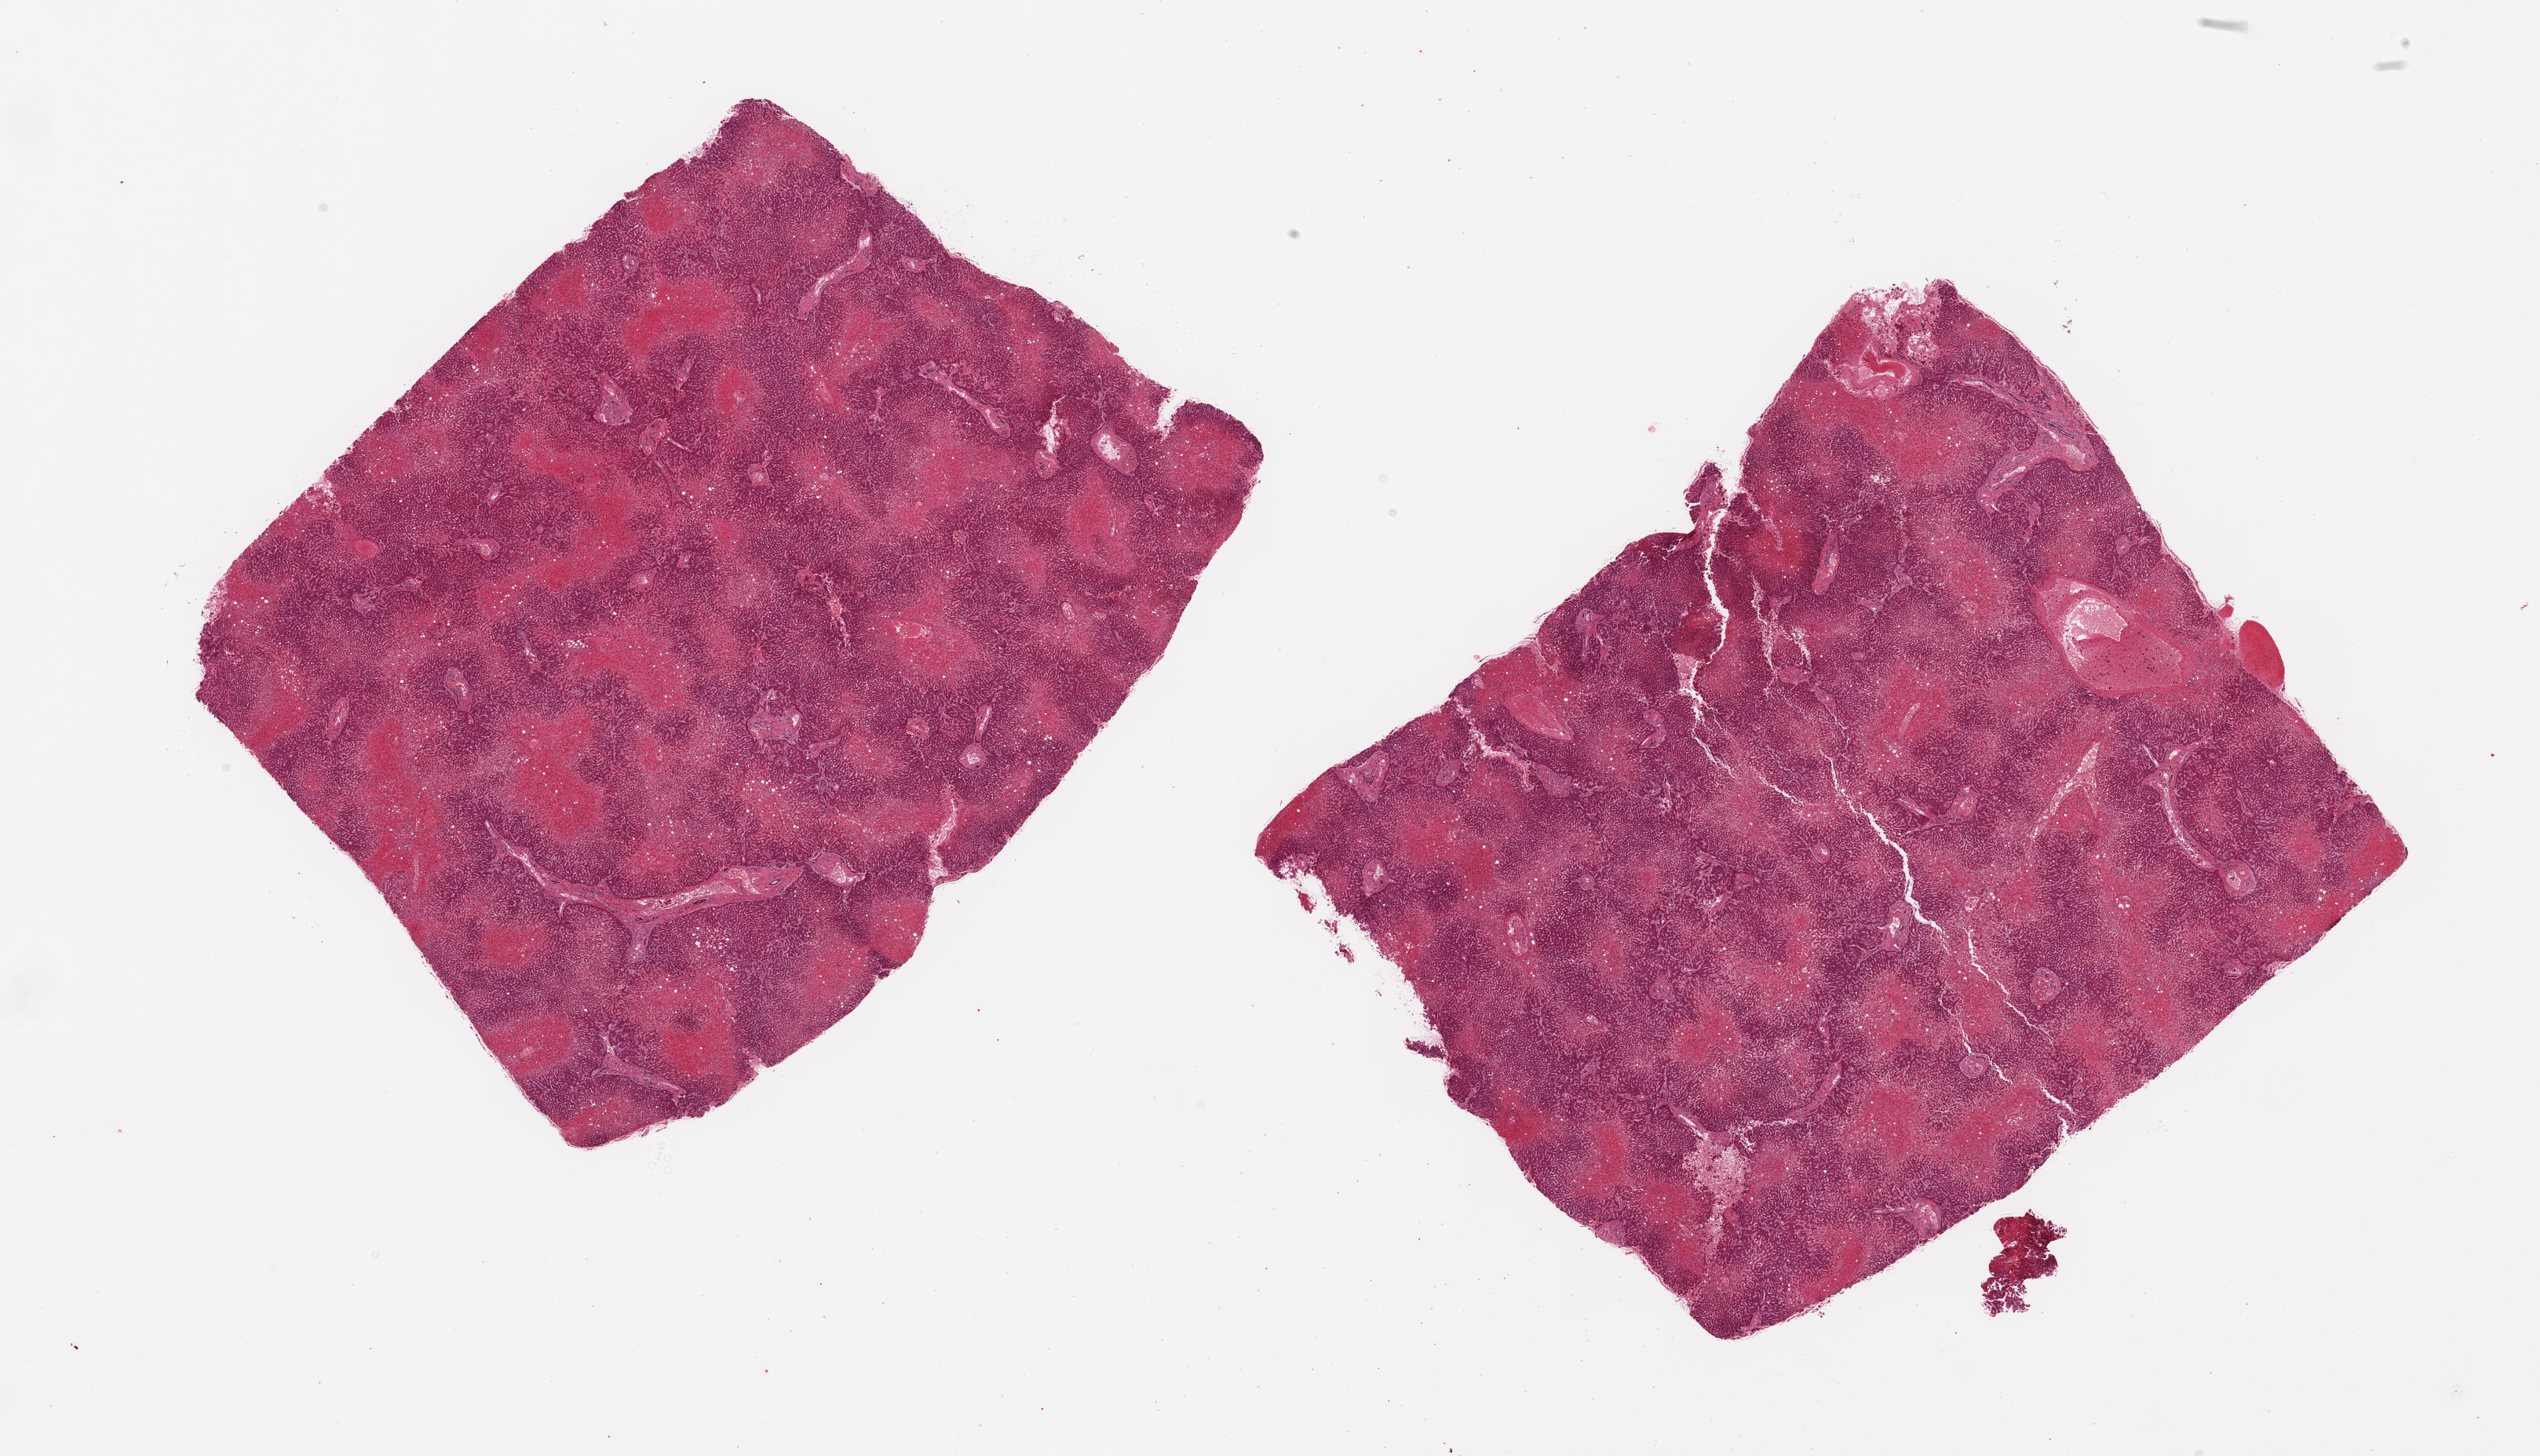
Digitized hematoxylin and eosin (H&E)-stained section — shown as a low-resolution overview of the whole scanned area (about 25.6 x 14.7 mm, from a 20x scan). PAXgene-fixed, paraffin-embedded tissue. Section of liver (target tissue). Tissue donor sample.
Reviewer comment on this tissue sample: 2 pieces; severe central passive congestion with liver cell degeneration.